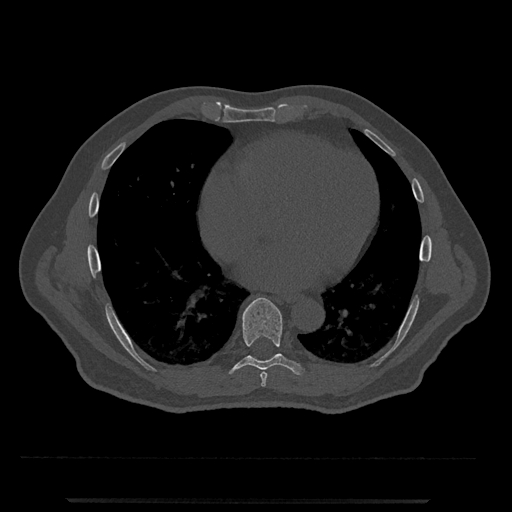
CT including the spine, one axial slice; 120 kVp; bone window (W 1800 / L 400 HU); 512 × 512 image matrix. Patient: male, 63 years. Case-level facts recorded for this patient, not image findings: primary cancer: prostate.
Annotated regions visible in this slice (semi-automatic segmentation, software-assisted and operator-edited):
- T7 vertebra: bounding box [x1, y1, x2, y2] px = [260, 372, 268, 387]
- T8 vertebra: [228, 298, 305, 375]